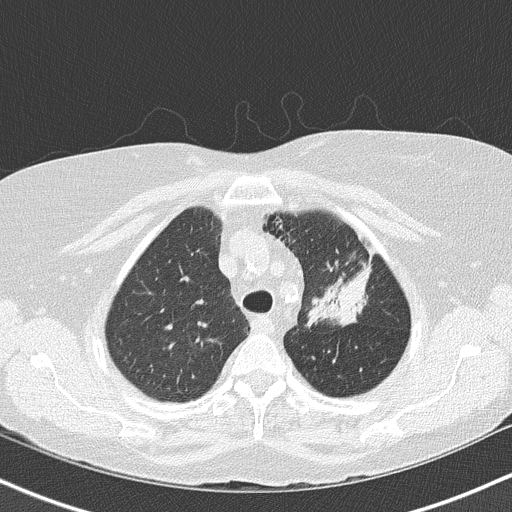
Low-dose screening chest CT, one axial slice; position 119 of 147 along the scan axis; reconstruction kernel B50f; lung window (W 1500 / L -600 HU); 2 mm slice thickness; 512 × 512 image matrix, field of view 320 × 320 mm.
Structures marked on this image (manually delineated by an expert):
- lesion 1 (tumor, upper lobe of left lung): bounding box <307,265,369,325> (left, top, right, bottom; pixels)